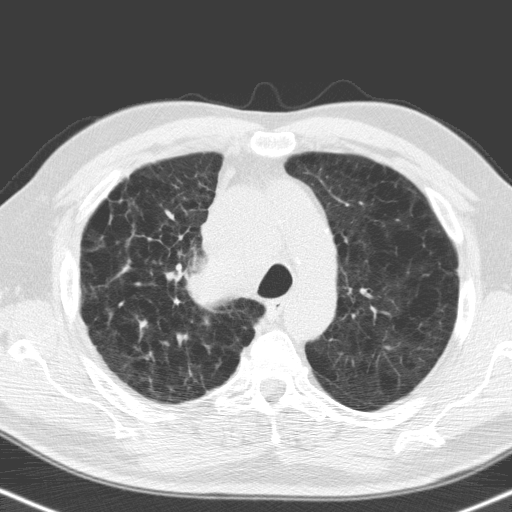
Low-dose screening chest CT, one axial slice; slice 124 of 160 in the series (ordered by position); lung window (W 1500 / L -600 HU); 512 × 512 image matrix.
Structures marked on this image (expert manual segmentation):
- lesion 1 (tumor, hilum of right lung): bounding box <188,256,240,307> (left, top, right, bottom; pixels)